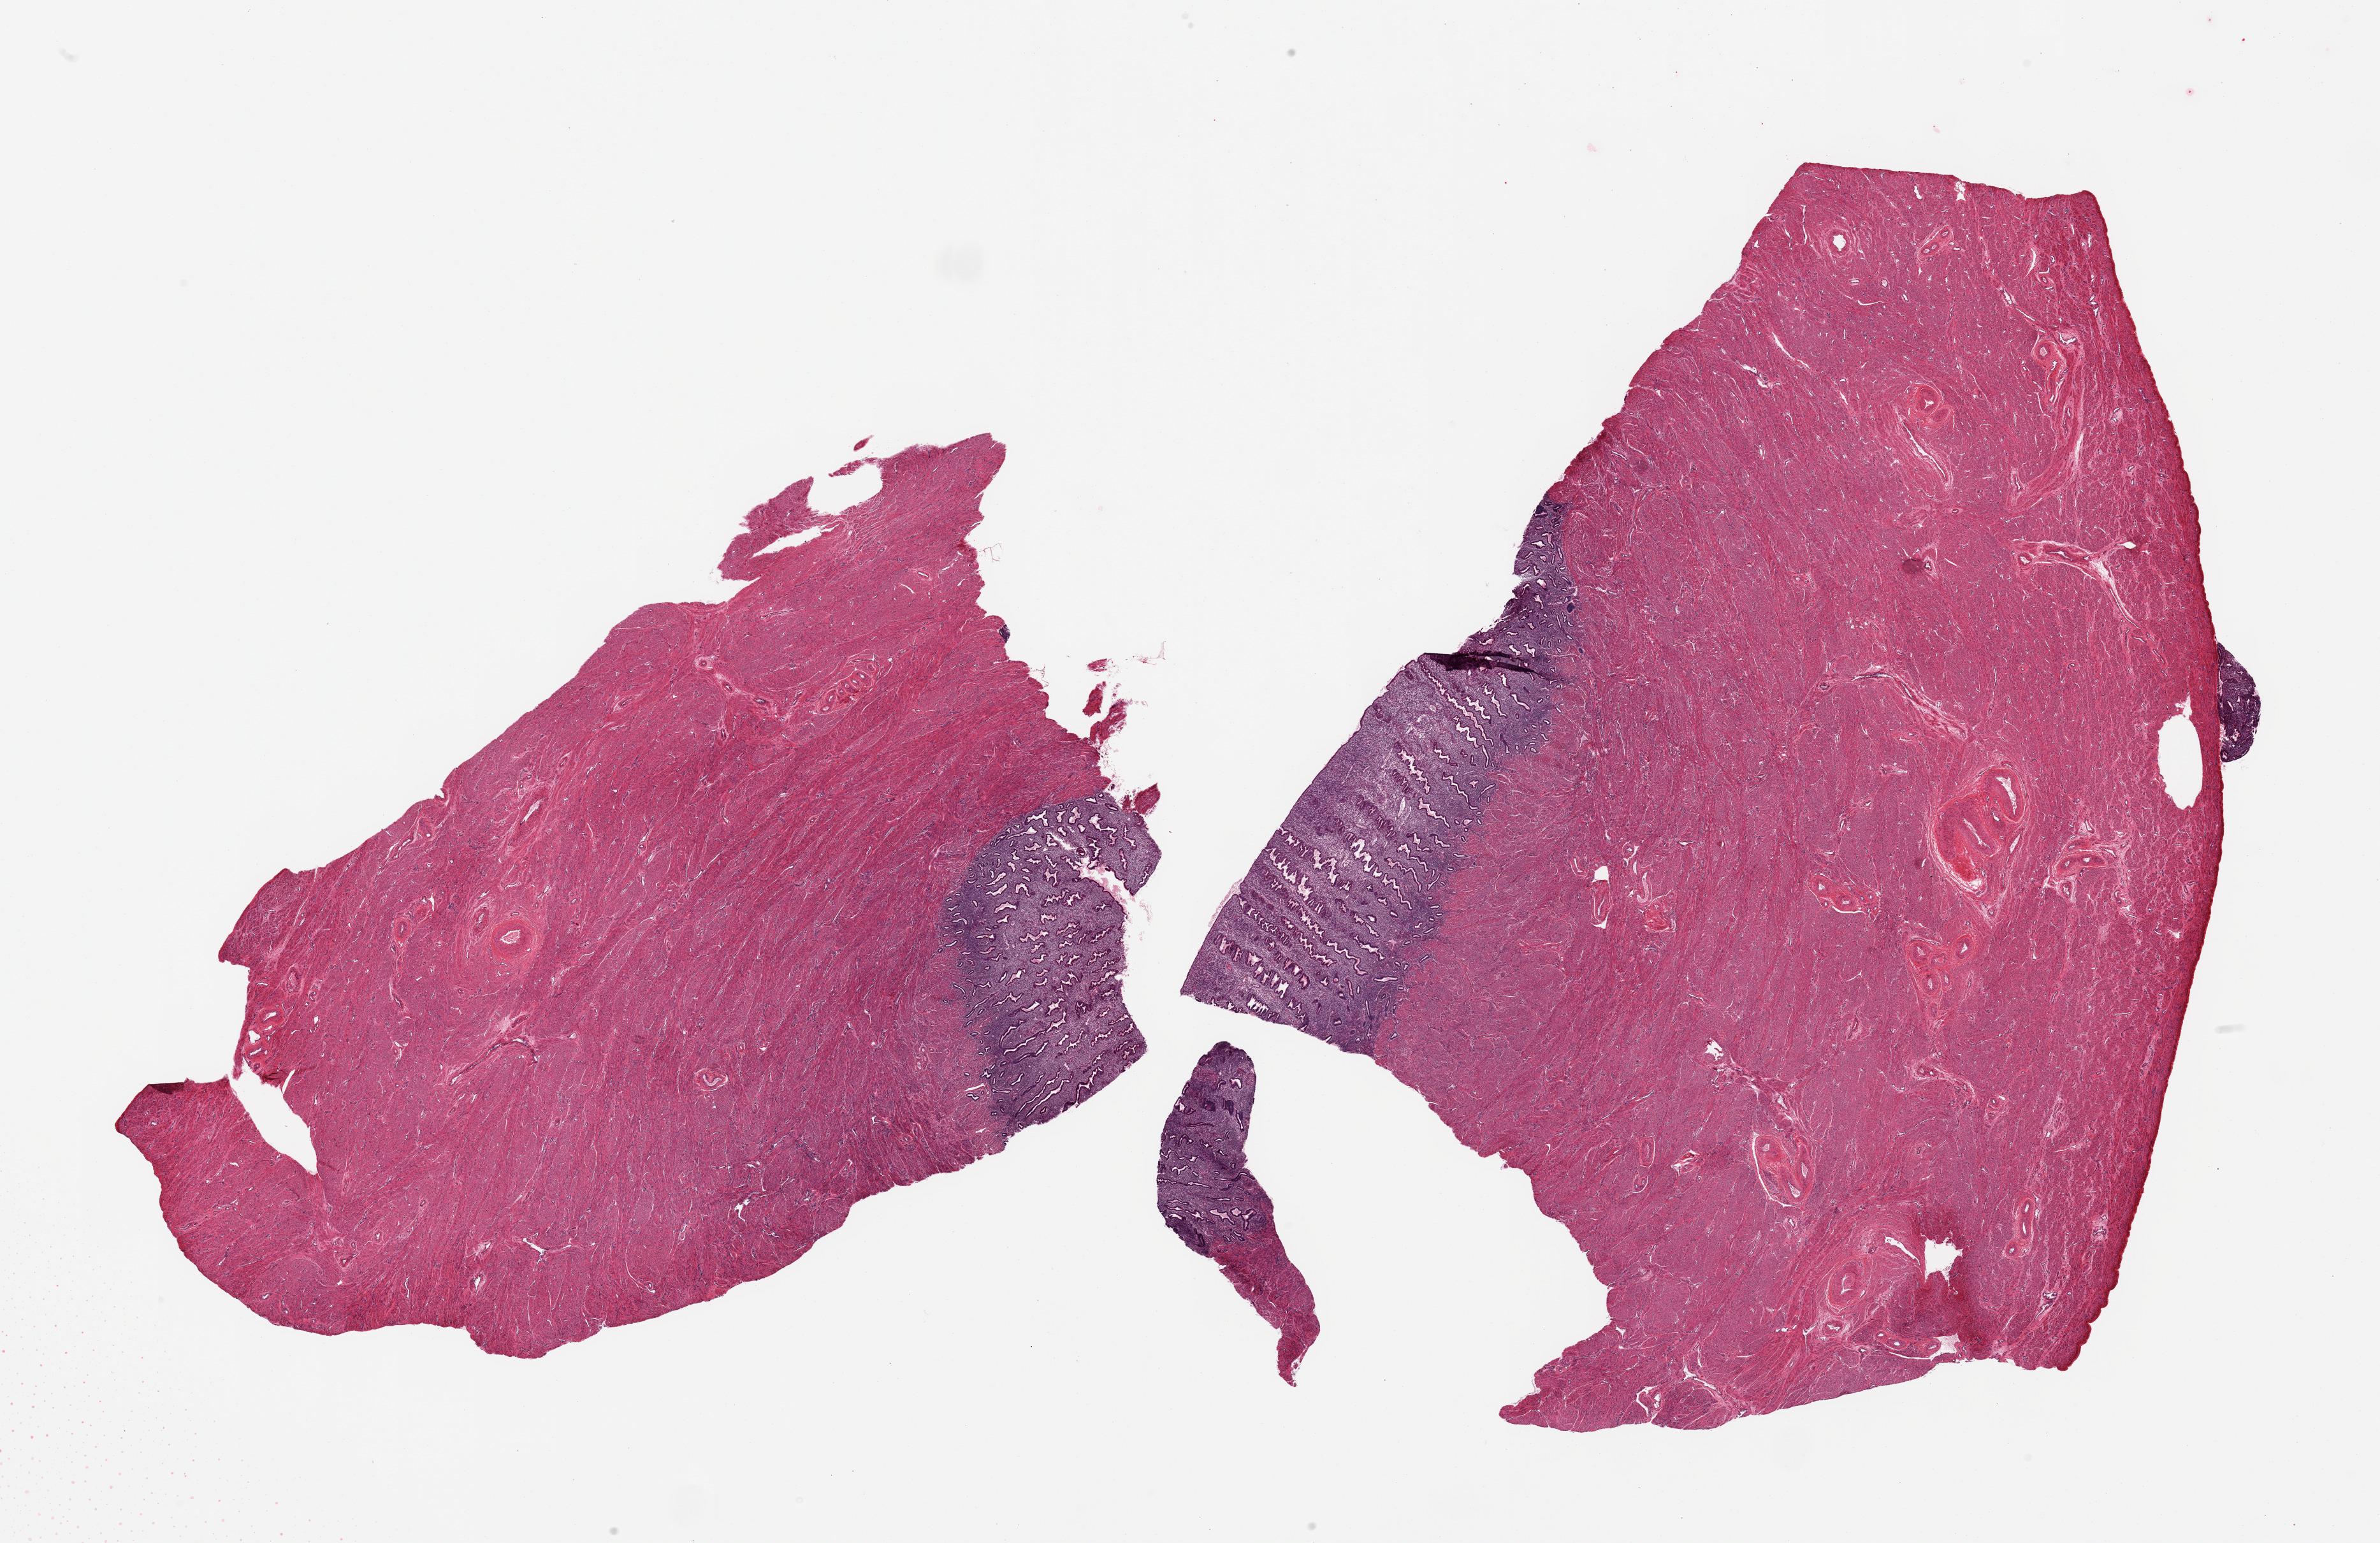
H&E whole-slide image, low-resolution overview of the scanned area, about 29.5 x 19.1 mm; PAXgene-fixed, paraffin-embedded tissue; sampled site (target tissue): uterus; donor tissue sample. Female donor.
* reviewer comment on this tissue sample: 2 pieces, mainly myometrium; 2-3mm strip of endometrium-glands/stroma, good specimen